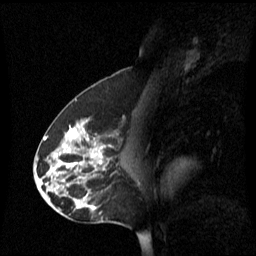
Breast MRI (dynamic contrast-enhanced), one sagittal slice. Slice 33 of 60 in the series (ordered by position). Dynamic contrast-enhanced series, image 2 of 3 at this slice position (ordered by acquisition). 1.5 T. TE 4.2 ms, TR 8.4 ms. 2.2 mm slice thickness. 256 × 256 image matrix. Female patient, age 45 years. From the clinical record (not read from this slice): setting: breast cancer imaged before/during neoadjuvant chemotherapy; receptor status: HR-positive, HER2-negative.
Annotated regions visible in this slice (semi-automatic segmentation, software-assisted and operator-edited):
- analysis volume of interest (the breast-tissue region the enhancement analysis was run in; not a lesion): bounding box (x1, y1, x2, y2) in pixels: (38, 120, 133, 221)
- tumour enhancement mask (voxels above the 70 % enhancement threshold inside the analysis volume of interest): (54, 124, 105, 209)